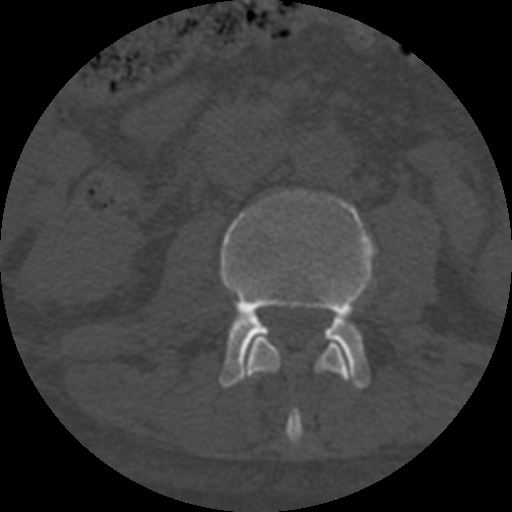
CT including the spine, one axial slice. Slice 243 of 708 in the series (ordered by position). 120 kVp. One of 3 acquisitions stored at this slice position. Bone window (W 1800 / L 400 HU). 1.25 mm slice thickness. 512 × 512 image matrix, field of view 160 × 160 mm. Patient age 55 years. From the clinical record (not read from this slice): primary cancer: colon; vertebrae with lytic lesions (as recorded): T12, L1, L5.
Annotated regions visible in this slice (semi-automatic segmentation, software-assisted and operator-edited):
- L2 vertebra: box from (x=245, y=337) to (x=349, y=447) px
- L3 vertebra: (x=219, y=189)–(x=374, y=388)